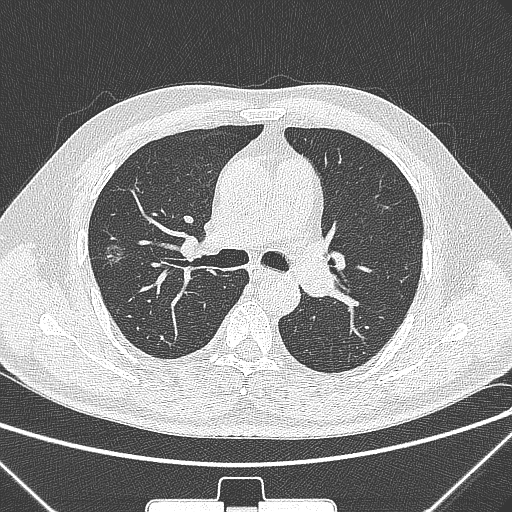
Chest CT, one axial slice; slice 193 of 320 in the series (ordered by position); 120 kVp; lung window (W 1500 / L -600 HU); 512 × 512 image matrix, field of view 350 × 350 mm. Male patient, age 58 years. Case-level facts recorded for this patient, not image findings: clinical TNM (as recorded): T1c N0 M0; histopathological grade: G2.
Annotated regions visible in this slice (bounding box drawn by a radiologist):
- lung tumour (recorded histology: adenocarcinoma): bounding box [x1, y1, x2, y2] px = [98, 238, 129, 272]